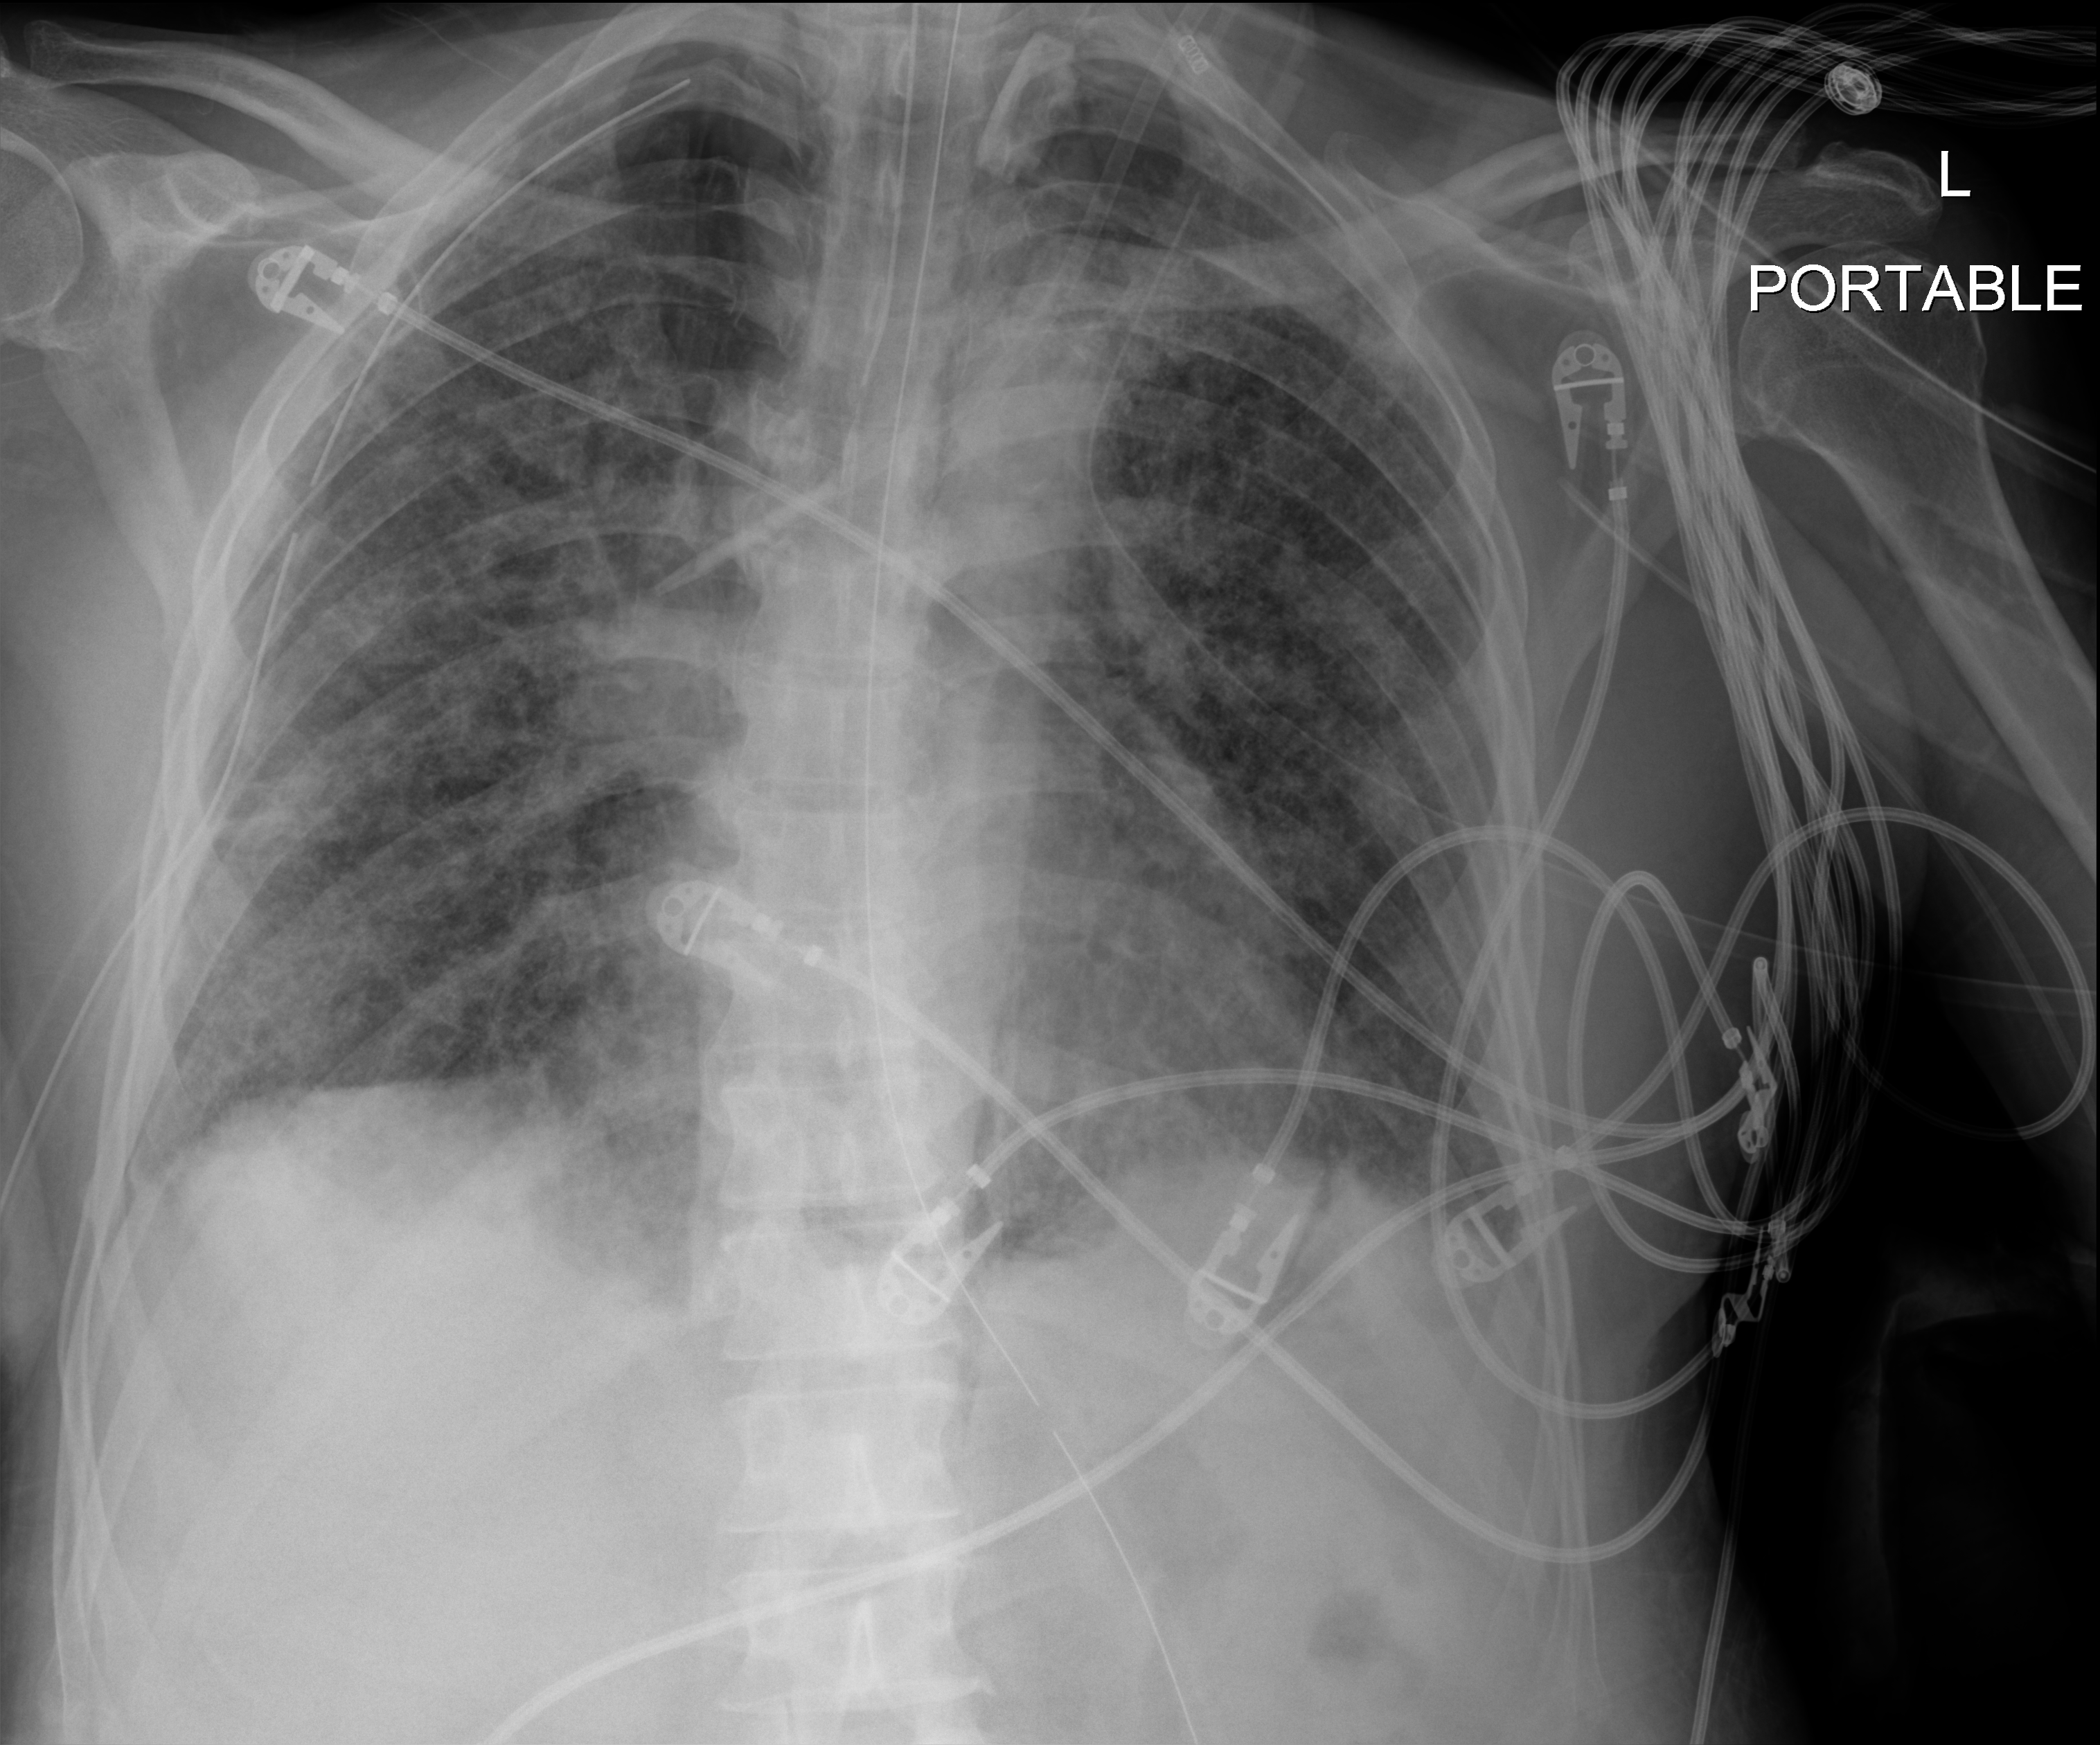
Portable chest radiograph, anteroposterior (AP) projection. Male patient hospitalised with COVID-19, age 60–74 years.
Hospital-stay facts (about this admission, not read from this image; timing relative to this image not recorded): length of hospital stay: 65 days; mechanically ventilated during this hospital stay: yes.